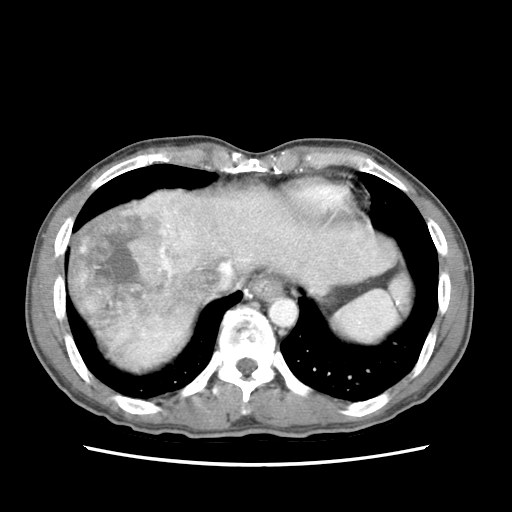
Contrast-enhanced abdominal CT (liver protocol), one axial slice; position 64 of 79 along the scan axis; reconstruction kernel STANDARD; soft-tissue window (W 400 / L 40 HU); 512 × 512 image matrix, field of view 320 × 320 mm. From the clinical record (not read from this slice): diagnosis: hepatocellular carcinoma (patient treated with transarterial chemoembolisation; whether this scan precedes or follows treatment is not stated here); TNM stage (as recorded): Stage-IIIB; Child-Pugh class: A; tumour differentiation: moderately differentiated; tumour nodularity: multinodular.
Outlined on this slice (semi-automatically segmented with operator editing):
- abdominal aorta: bounding box <270,299,296,327> (left, top, right, bottom; pixels)
- liver parenchyma outside the tumour (the mass and vessels are separate outlines, so this box may not span the whole liver): <69,184,396,370>
- mass: <69,189,206,362>
- liver vessels: <206,226,279,279>